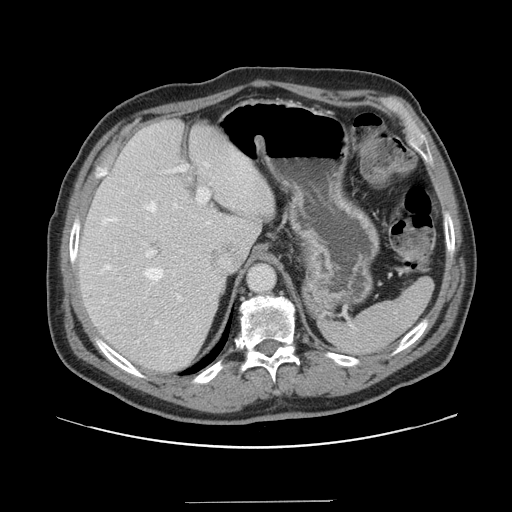
Contrast-enhanced abdominal CT, one axial slice; slice 109 of 151 in the series (ordered by position); intravenous contrast given; soft-tissue window (W 400 / L 40 HU); 512 × 512 image matrix. Male patient, age 63 years. Case-level facts recorded for this patient, not image findings: diagnosis: colorectal cancer liver metastases, imaged before liver resection; multiple liver metastases: no; largest metastasis: 2.1 cm; chemotherapy before resection: no.
Annotated regions visible in this slice (manually delineated by an expert):
- hepatic veins: bounding box (x1, y1, x2, y2) in pixels: (102, 164, 208, 281)
- liver: (78, 119, 274, 373)
- planned liver remnant (the part of the liver to remain after resection): (78, 119, 266, 373)
- portal vein (with intrahepatic branches): (145, 165, 210, 300)